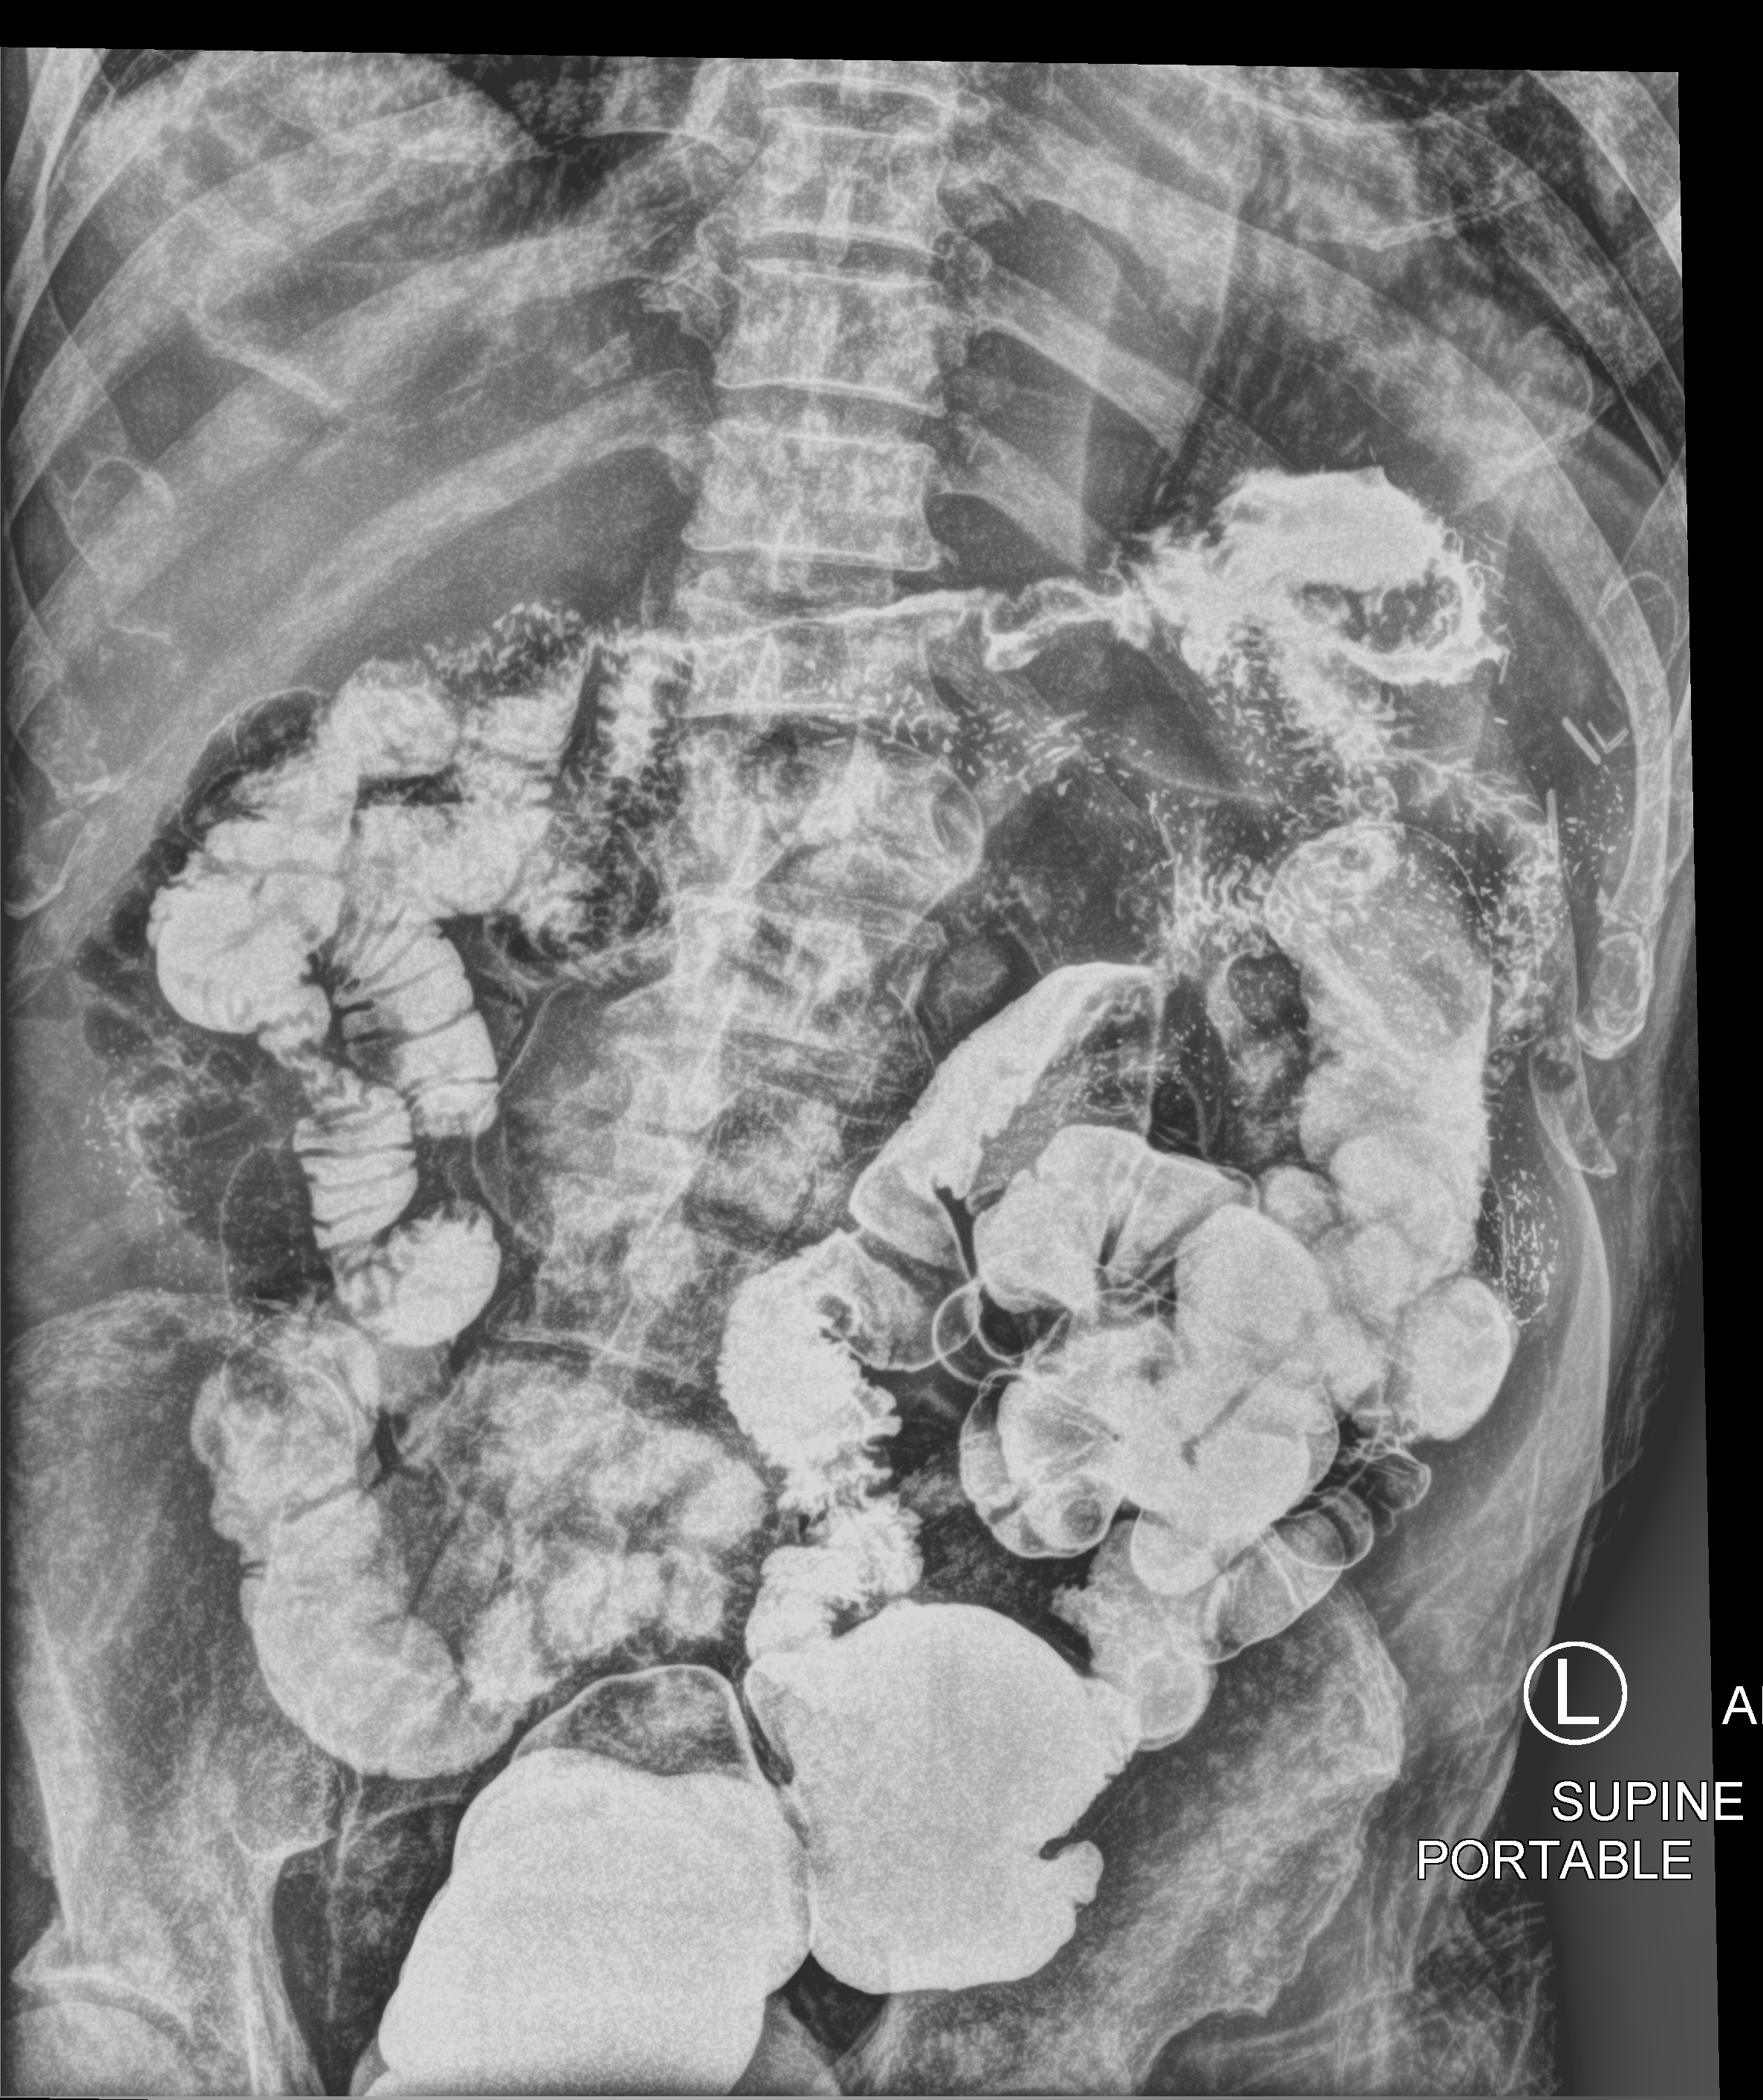
Bedside abdomen radiograph (computed radiography); anteroposterior (AP) projection. Male patient hospitalised with COVID-19, age 75–90 years.
From the hospital-stay record, not from the radiograph (when in the stay this image was taken is not recorded):
- mechanically ventilated during this hospital stay: no
- admitted to intensive care during this hospital stay: no